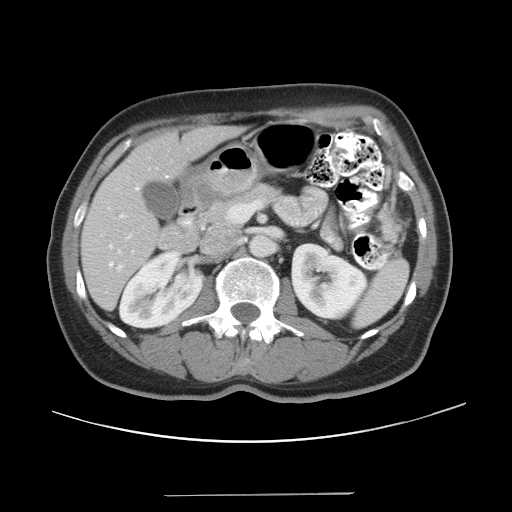
Contrast-enhanced abdominal CT, one axial slice; position 18 of 43 along the scan axis; reconstruction kernel STANDARD; 120 kVp; intravenous contrast given; soft-tissue window (W 400 / L 40 HU); 5 mm slice thickness; 512 × 512 image matrix, field of view 409 × 409 mm. Male patient, age 65 years. Case-level facts recorded for this patient, not image findings: diagnosis: colorectal cancer liver metastases, imaged before liver resection; multiple liver metastases: no; largest metastasis: 3.8 cm.
Structures marked on this image (expert manual segmentation):
- hepatic veins: bounding box <107,186,140,266> (left, top, right, bottom; pixels)
- liver: <83,127,237,308>
- planned liver remnant (the part of the liver to remain after resection): <83,127,237,308>
- portal vein (with intrahepatic branches): <101,214,126,236>